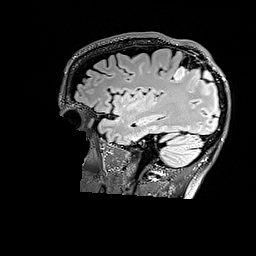
Brain MRI from a brain-tumour surgery series, one sagittal slice; slice 124 of 176 in the series (ordered by position); T2 FLAIR; 256 × 256 image matrix. From the clinical record (not read from this slice): histopathology: Astrocytoma; WHO grade: 3; IDH mutation: yes; tumour location: Right Parietal.
Structures marked on this image (outlined manually by an expert reader):
- tumour: bounding box (x1, y1, x2, y2) in pixels: (174, 66, 209, 80)